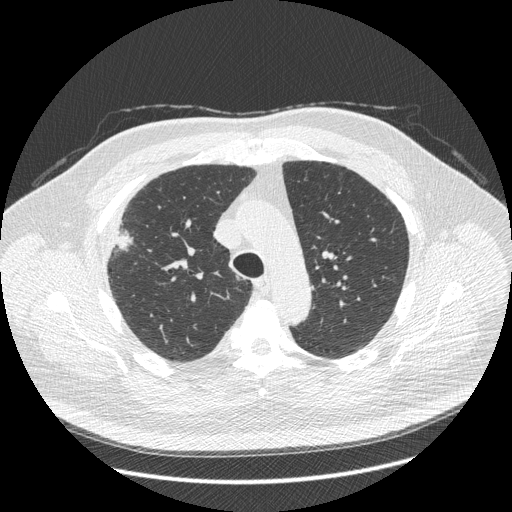
Axial slice from a low-dose chest CT screening exam. Third screening round (two years after baseline). Lung window (W 1500 / L -600 HU). 1.25 mm slice thickness. Standard (soft-tissue) reconstruction kernel (STANDARD). Slice 114 of 426 in the series. Male participant, aged 66 years at enrolment.
Expert reader's lesion annotation, box from (x=88, y=210) to (x=148, y=271) px. Reader record for this screening exam (exam-level; its link to the box is not recorded): non-calcified nodule or mass ≥4 mm, right upper lobe, 48 × 25 mm, spiculated (stellate) margins, soft tissue attenuation, pre-existing on the prior screen: no. Later outcome: lung cancer diagnosed 35 days after this screen — non-small cell carcinoma, right upper lobe, stage IV (AJCC 6th edition), 50 mm at pathology.